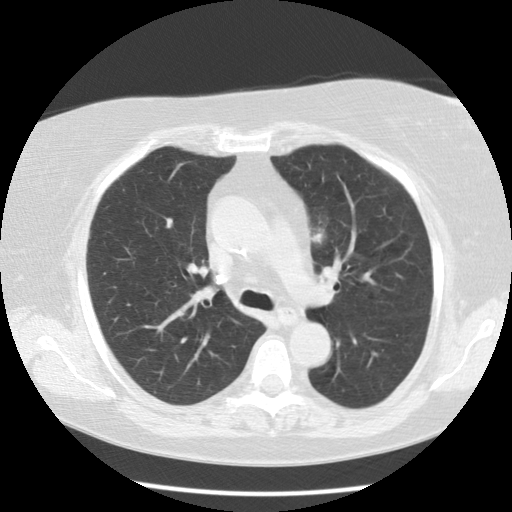
Low-dose screening chest CT, one axial slice. Position 77 of 109 along the scan axis. Reconstruction kernel STANDARD. Lung window (W 1500 / L -600 HU). 512 × 512 image matrix, field of view 334 × 334 mm.
Outlined on this slice (outlined manually by an expert reader):
- lesion 1 (tumor, upper lobe of left lung): bounding box [x1, y1, x2, y2] px = [312, 231, 324, 243]